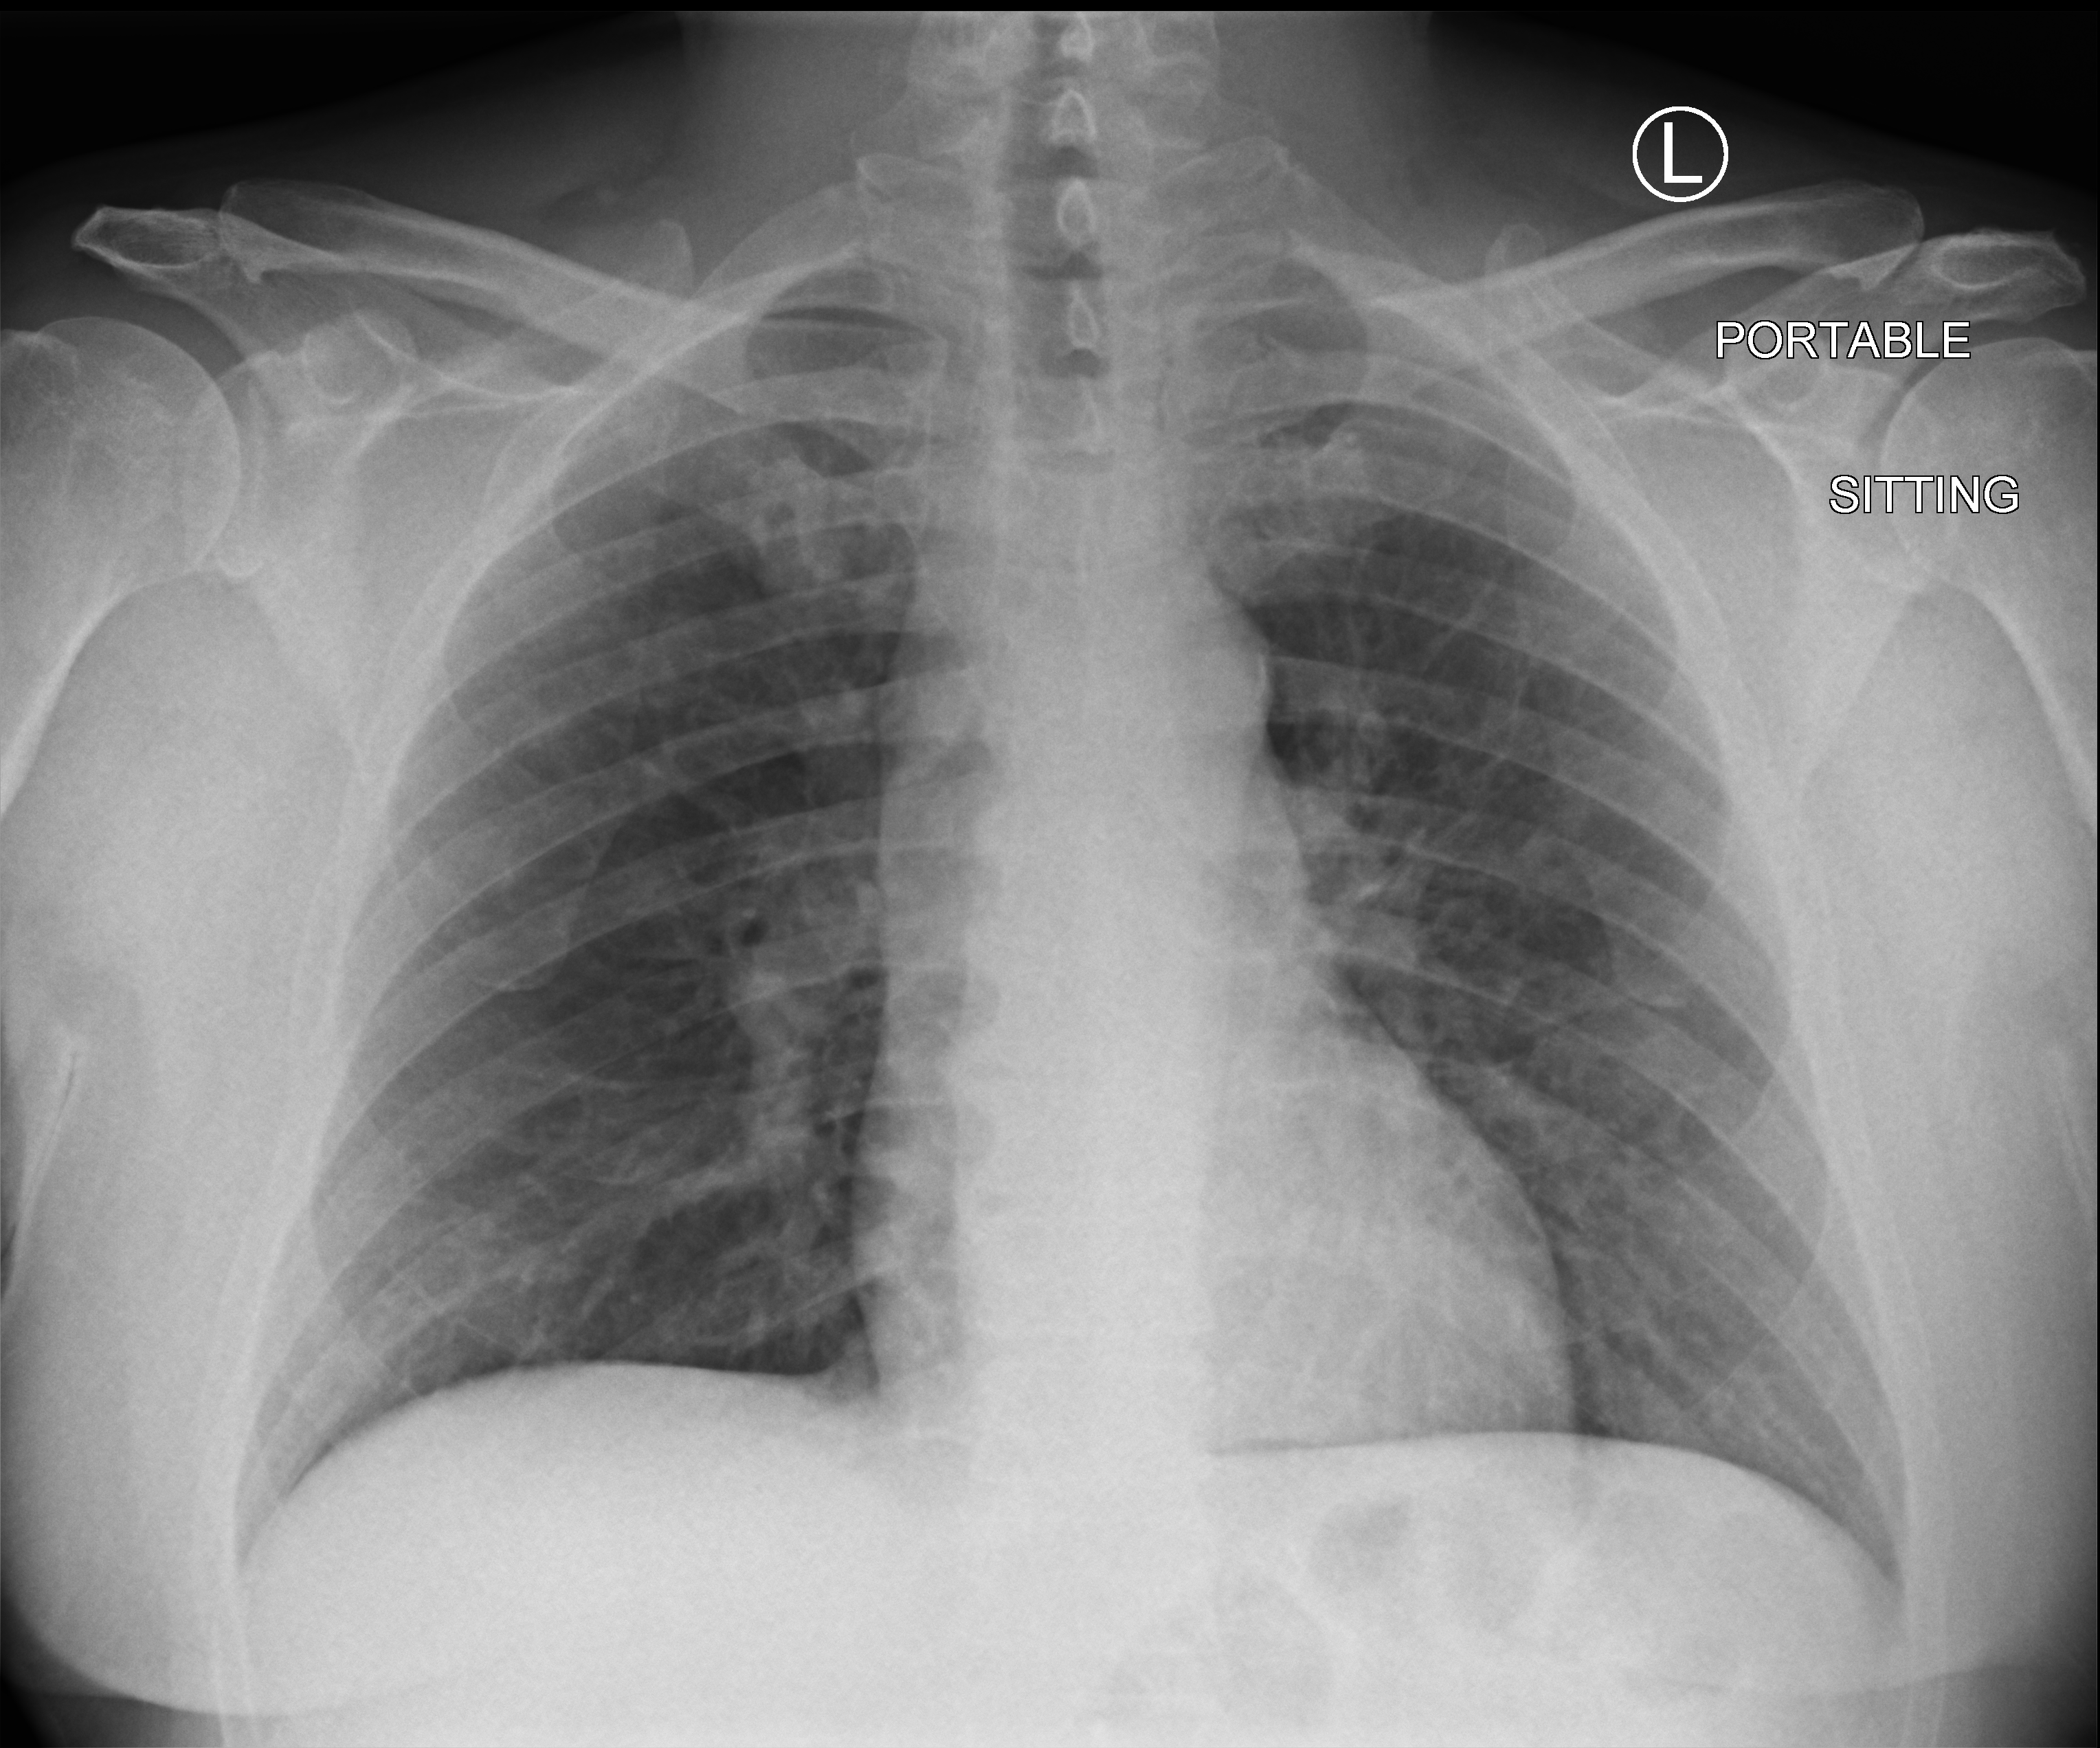
Chest X-ray (portable). Male patient hospitalised with COVID-19, age 18–59 years.
From the hospital-stay record, not from the radiograph (when in the stay this image was taken is not recorded):
- mechanically ventilated during this hospital stay: no
- length of hospital stay: 6 days